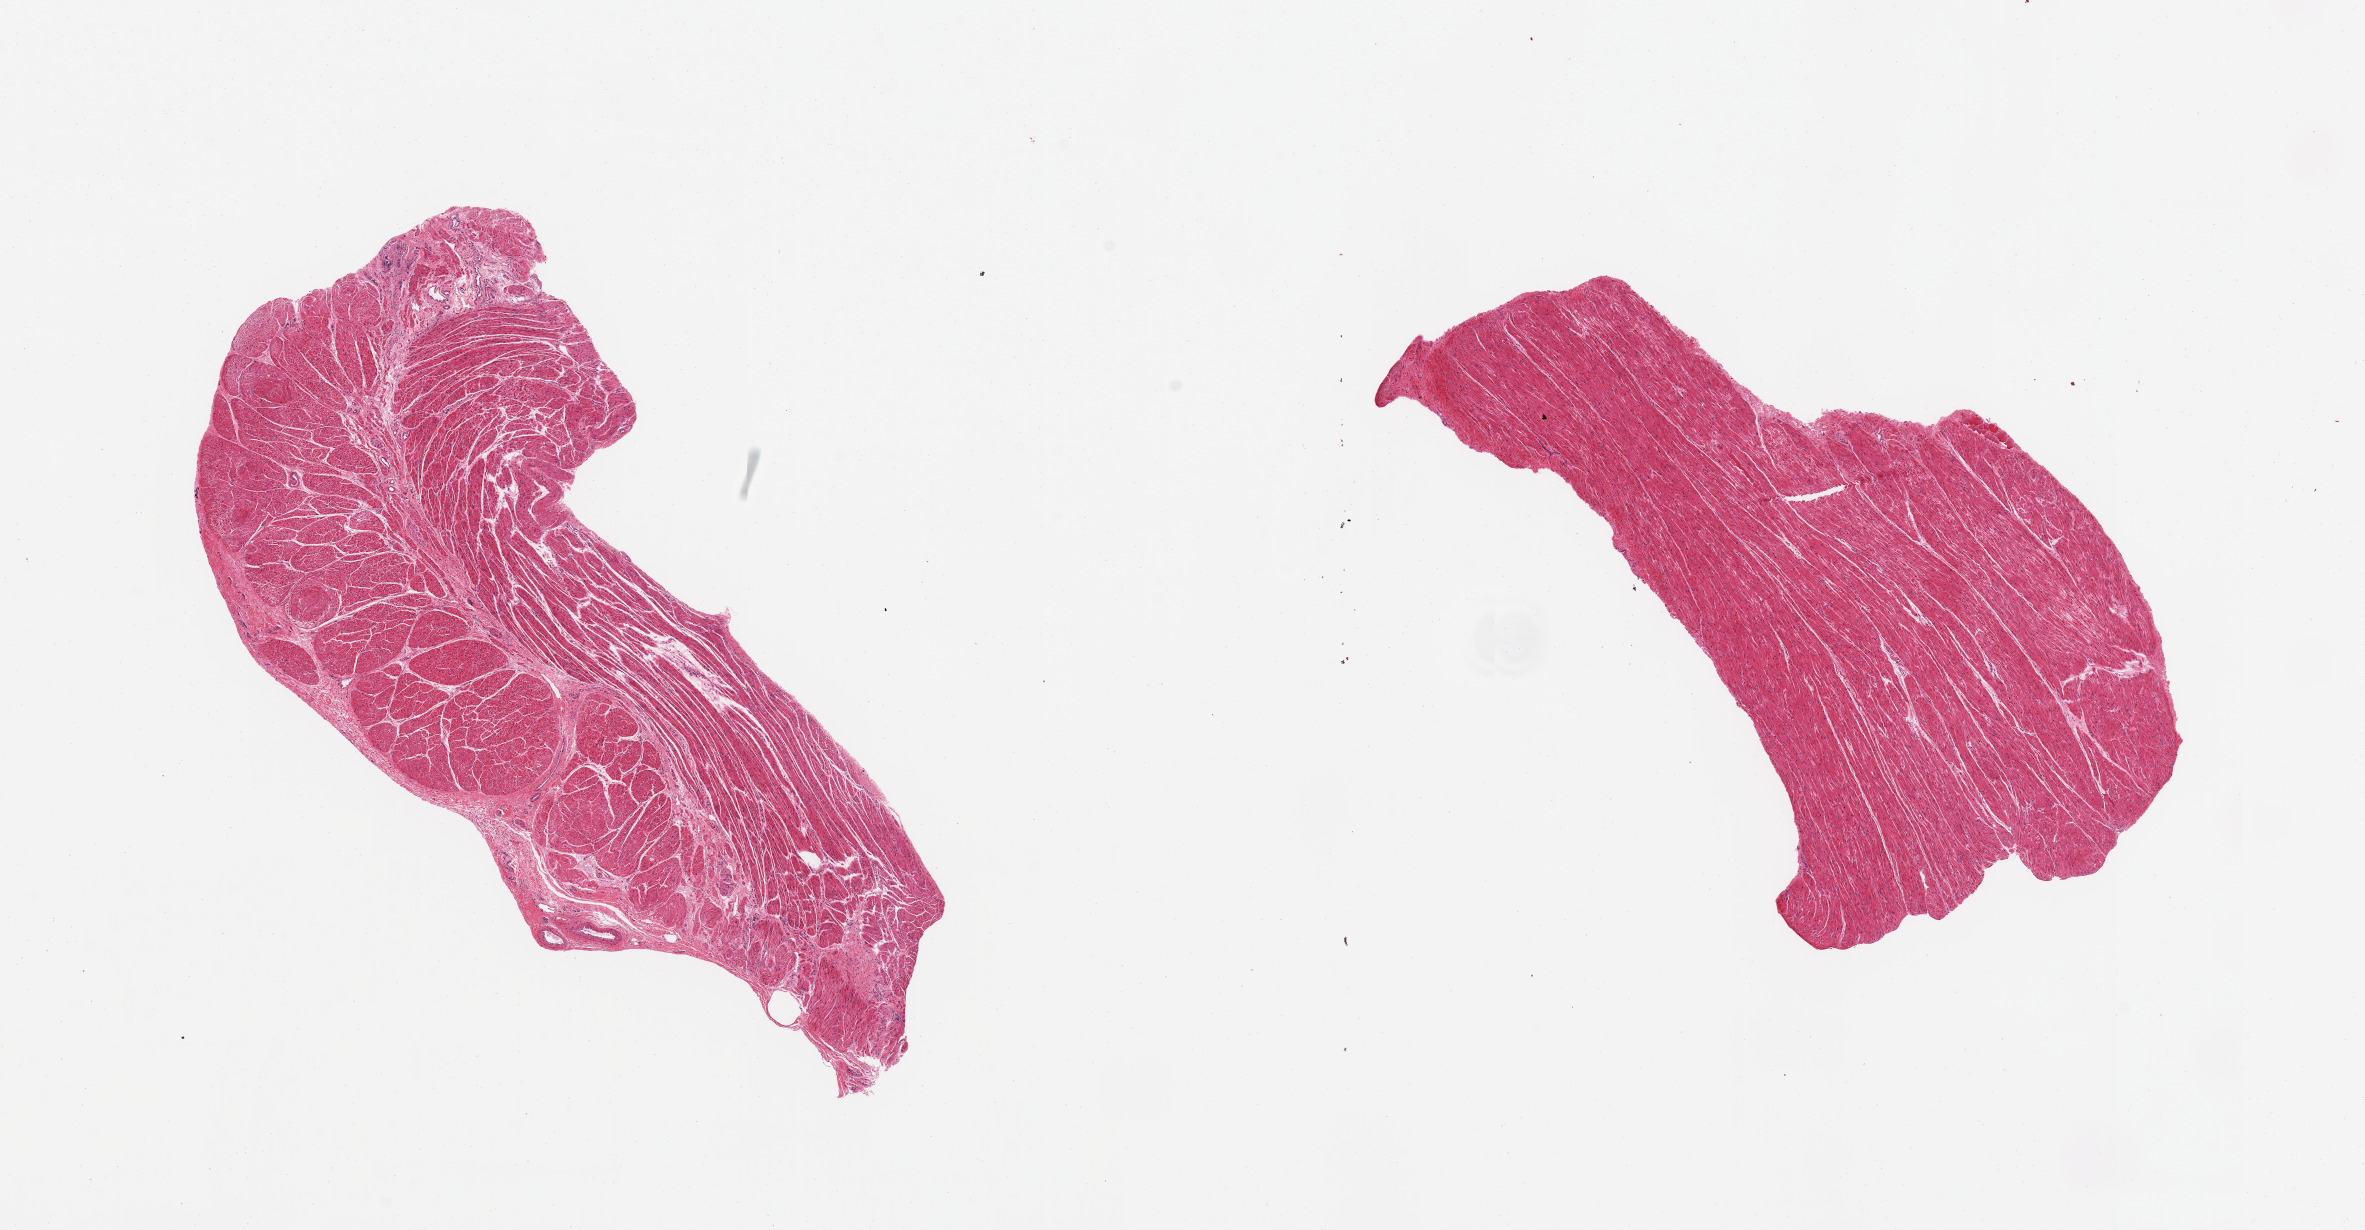
H&E whole-slide image, a low-resolution overview of the entire scanned area, about 18.7 x 9.7 mm (slide scanned at 20x). PAXgene-fixed paraffin-embedded (PFPE) section. Sampled site (target tissue): esophageal muscle. Tissue donor sample. Donor: male.
• review note (as recorded): 2 pieces, confirmed muscularis, mild reactive changes